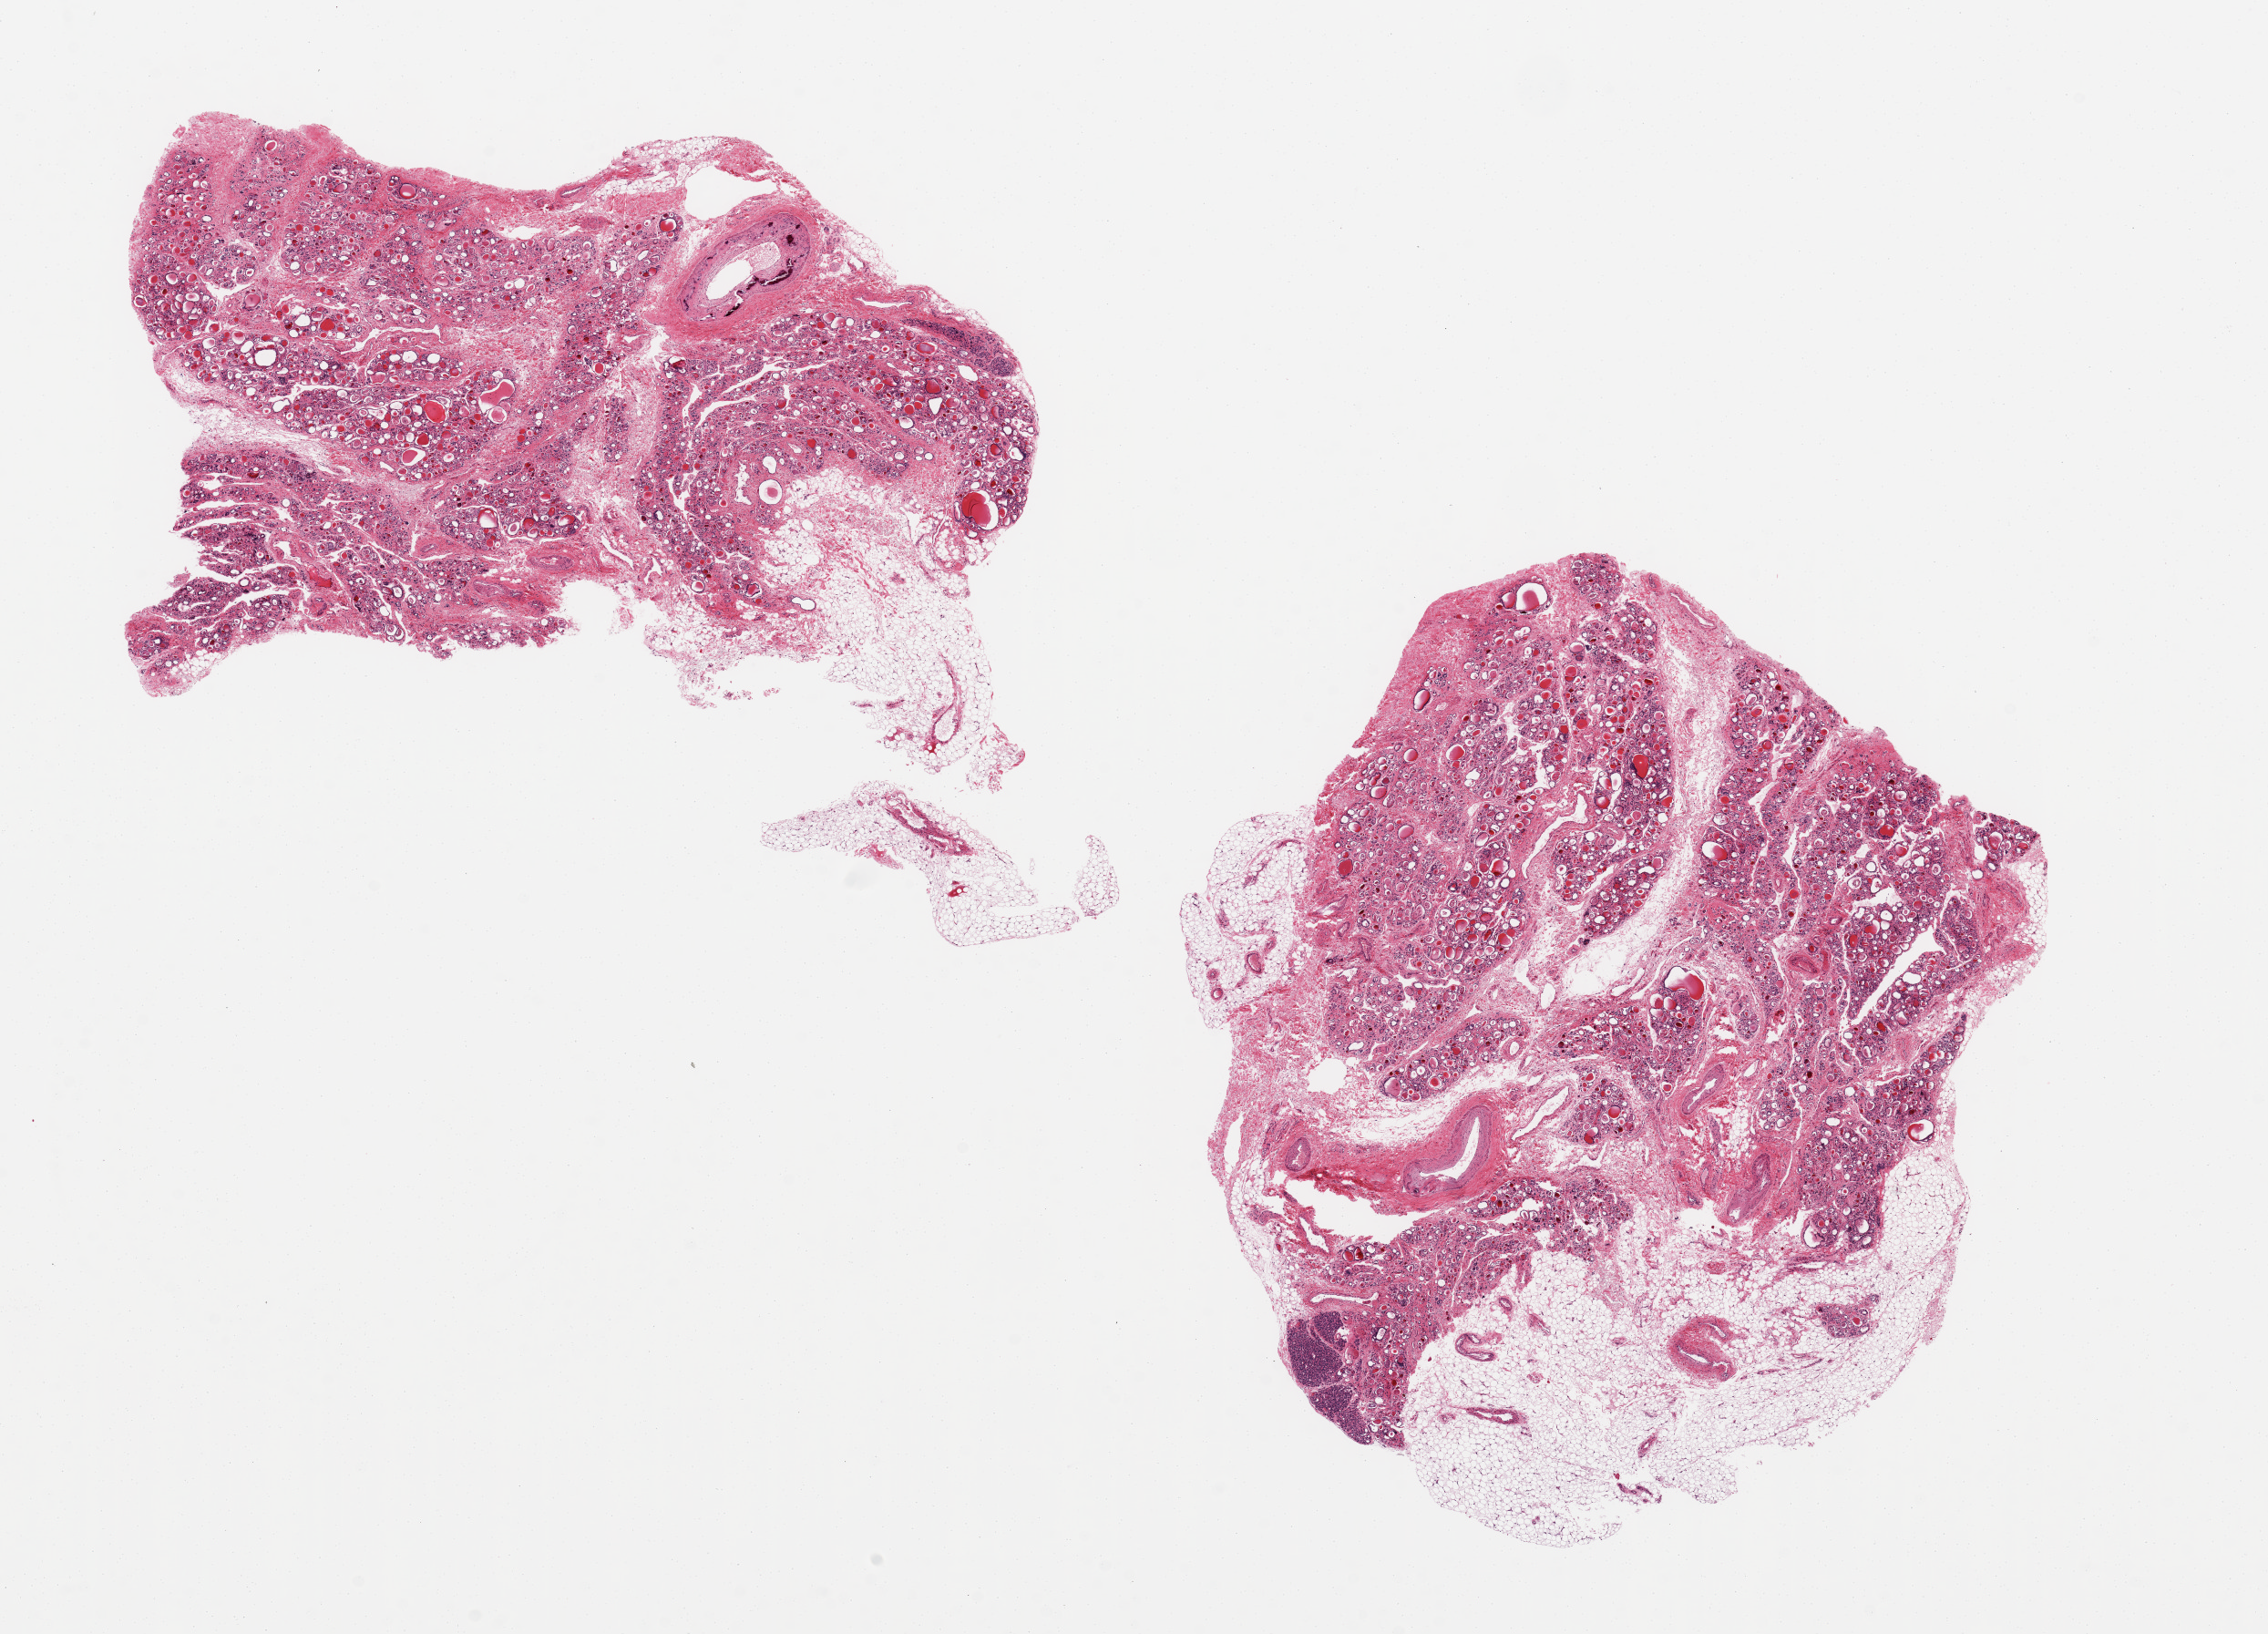
Whole-slide image, H&E stain — low-resolution overview of the scanned area, about 19.7 x 14.2 mm. PAXgene-fixed paraffin-embedded (PFPE) section. Target tissue: thyroid. Tissue donor sample.
- reviewer comment on this tissue sample: 2 pieces atrophic; possible small parathyroid focus 1mm